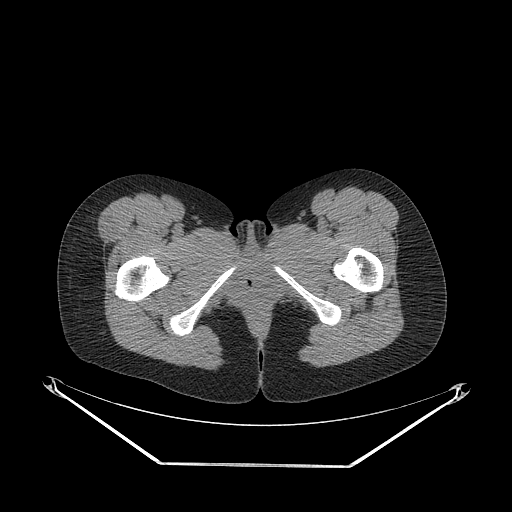
CT of an extremity soft-tissue mass (from a PET/CT study), one axial slice; slice 51 of 267 in the series (ordered by position); reconstruction kernel STANDARD; 140 kVp; soft-tissue window (W 400 / L 40 HU); 3.75 mm slice thickness; 512 × 512 image matrix, field of view 500 × 500 mm. Female patient. Case-level facts recorded for this patient, not image findings: histological type: synovial sarcoma; grade: intermediate; site of the primary tumour: right thigh.
Annotated regions visible in this slice (expert contour drawn on MRI and transferred to this co-registered scan by the dataset authors):
- gross tumour volume including surrounding oedema: bounding box (x1, y1, x2, y2) in pixels: (94, 219, 113, 241)
- gross tumour volume (mass): (94, 219, 113, 243)